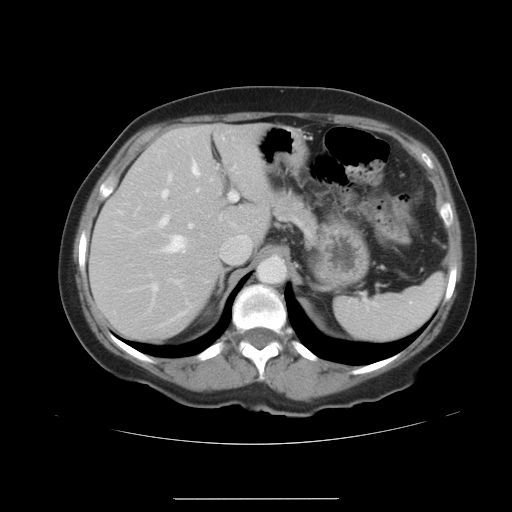
Contrast-enhanced abdominal CT, one axial slice; position 26 of 41 along the scan axis; 120 kVp; soft-tissue window (W 400 / L 40 HU); 5 mm slice thickness; 512 × 512 image matrix. Female patient, age 63 years. Case-level facts recorded for this patient, not image findings: diagnosis: colorectal cancer liver metastases, imaged before liver resection; multiple liver metastases: yes; largest metastasis: 1.5 cm; disease in both lobes: yes.
Annotated regions visible in this slice (manually delineated by an expert):
- hepatic veins: bounding box (x1, y1, x2, y2) in pixels: (164, 162, 199, 252)
- liver: (90, 124, 272, 343)
- planned liver remnant (the part of the liver to remain after resection): (90, 124, 272, 343)
- portal vein (with intrahepatic branches): (153, 191, 237, 290)